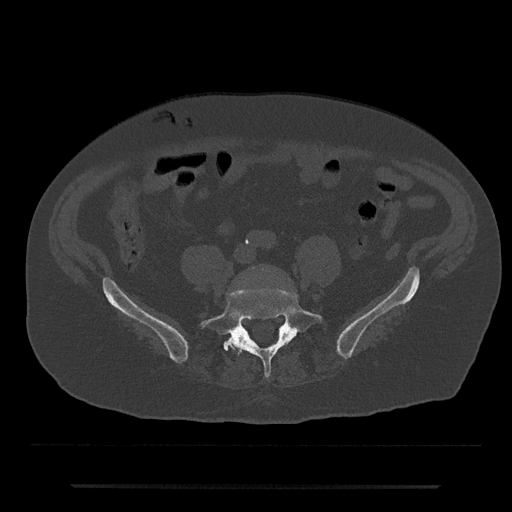
CT including the spine, one axial slice. Slice 295 of 797 in the series (ordered by position). Reconstruction kernel Br40s/3. 120 kVp. Bone window (W 1800 / L 400 HU). 0.5 mm slice thickness. 512 × 512 image matrix, field of view 434 × 434 mm. Male patient, age 80 years. From the clinical record (not read from this slice): primary cancer: prostate; vertebrae with lytic lesions (as recorded): L1, T11.
Annotated regions visible in this slice (semi-automatic segmentation, software-assisted and operator-edited):
- L5 vertebra: bounding box <201,288,322,378> (left, top, right, bottom; pixels)